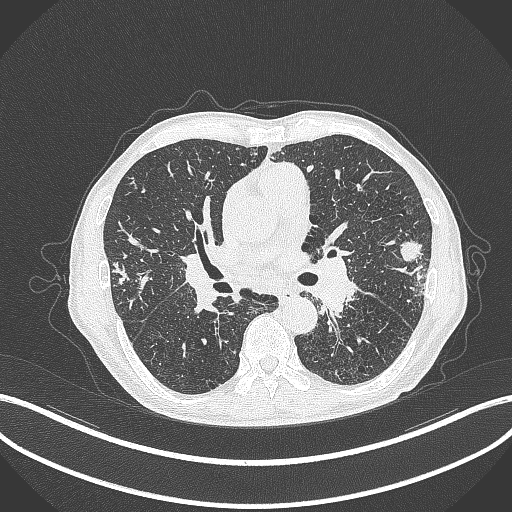
Chest CT, one axial slice. Slice 220 of 463 in the series (ordered by position). Reconstruction kernel B70f. 120 kVp. Lung window (W 1500 / L -600 HU). 512 × 512 image matrix, field of view 400 × 400 mm. Patient: male, 74 years. From the clinical record (not read from this slice): clinical TNM (as recorded): T2a N1 M0.
Outlined on this slice (bounding box drawn by a radiologist):
- lung tumour (recorded histology: adenocarcinoma): bounding box [x1, y1, x2, y2] px = [398, 236, 431, 261]